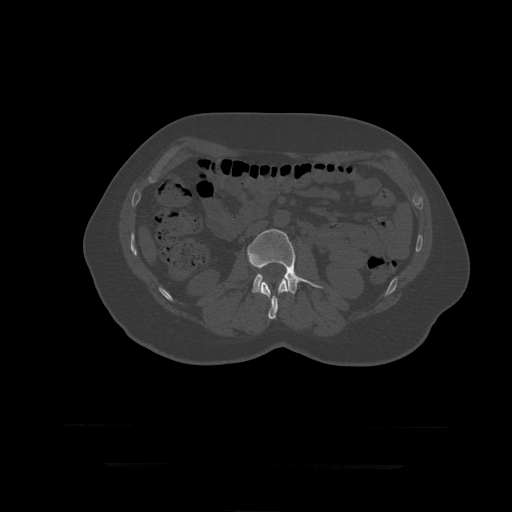
CT including the spine, one axial slice. Reconstruction kernel STANDARD. Bone window (W 1800 / L 400 HU). 1.25 mm slice thickness. 512 × 512 image matrix. Patient age 41 years. Case-level facts recorded for this patient, not image findings: primary cancer: breast.
Structures marked on this image (semi-automatic segmentation, software-assisted and operator-edited):
- L2 vertebra: bounding box (x1, y1, x2, y2) in pixels: (260, 278, 288, 320)
- L3 vertebra: (247, 229, 323, 294)